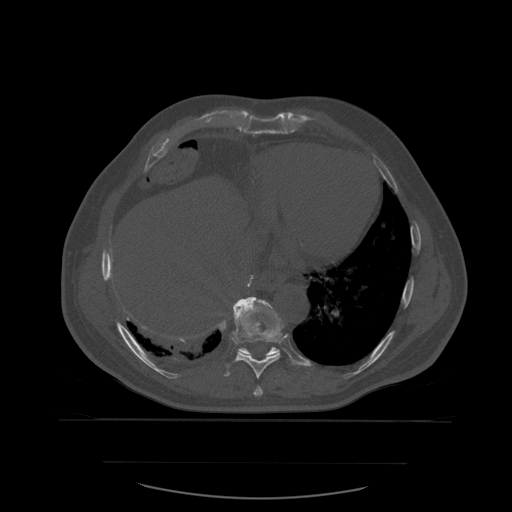
CT including the spine, one axial slice; position 335 of 590 along the scan axis; bone window (W 1800 / L 400 HU); 1.25 mm slice thickness; 512 × 512 image matrix, field of view 479 × 479 mm. Patient age 71 years. From the clinical record (not read from this slice): primary cancer: lung; vertebrae with lytic lesions (as recorded): T1, T2, L5, S1.
Outlined on this slice (semi-automatically segmented with operator editing):
- T10 vertebra: box from (x=233, y=297) to (x=285, y=357) px
- T8 vertebra: (x=254, y=386)–(x=264, y=397)
- T9 vertebra: (x=224, y=297)–(x=284, y=380)